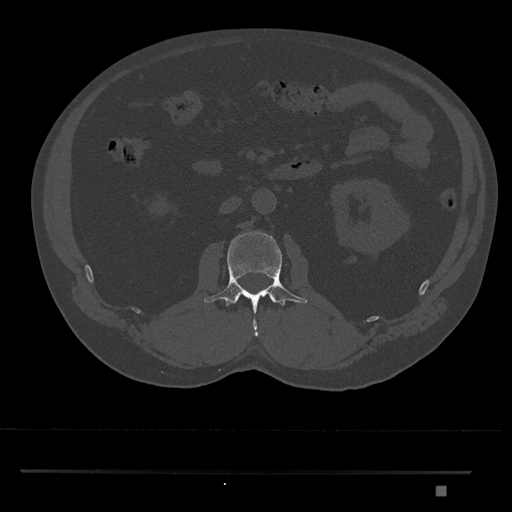
CT including the spine, one axial slice; slice 755 of 1134 in the series (ordered by position); 120 kVp; bone window (W 1800 / L 400 HU); 0.5 mm slice thickness; 512 × 512 image matrix. Male patient, age 65 years. From the clinical record (not read from this slice): primary cancer: prostate.
Annotated regions visible in this slice (semi-automatically segmented with operator editing):
- L2 vertebra: box from (x=204, y=230) to (x=307, y=337) px